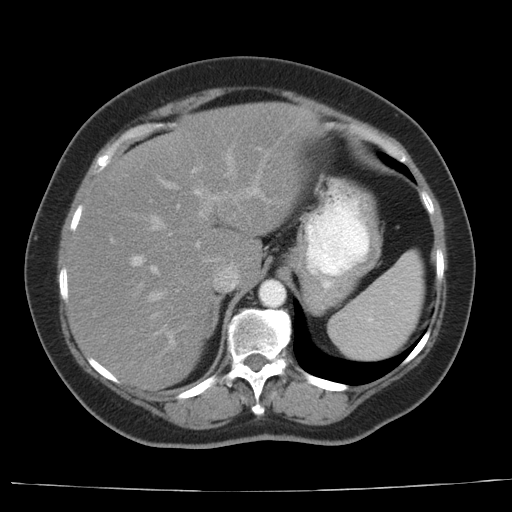
Contrast-enhanced abdominal CT, one axial slice. Slice 25 of 44 in the series (ordered by position). Reconstruction kernel AA-1. 140 kVp. Intravenous contrast given. Soft-tissue window (W 400 / L 40 HU). 512 × 512 image matrix. Female patient. From the clinical record (not read from this slice): diagnosis: colorectal cancer liver metastases, imaged before liver resection; multiple liver metastases: yes; largest metastasis: 1.8 cm; chemotherapy before resection: yes.
Structures marked on this image (expert manual segmentation):
- hepatic veins: bounding box <149,152,234,317> (left, top, right, bottom; pixels)
- liver: <66,103,319,390>
- planned liver remnant (the part of the liver to remain after resection): <93,103,319,286>
- portal vein (with intrahepatic branches): <110,153,272,345>